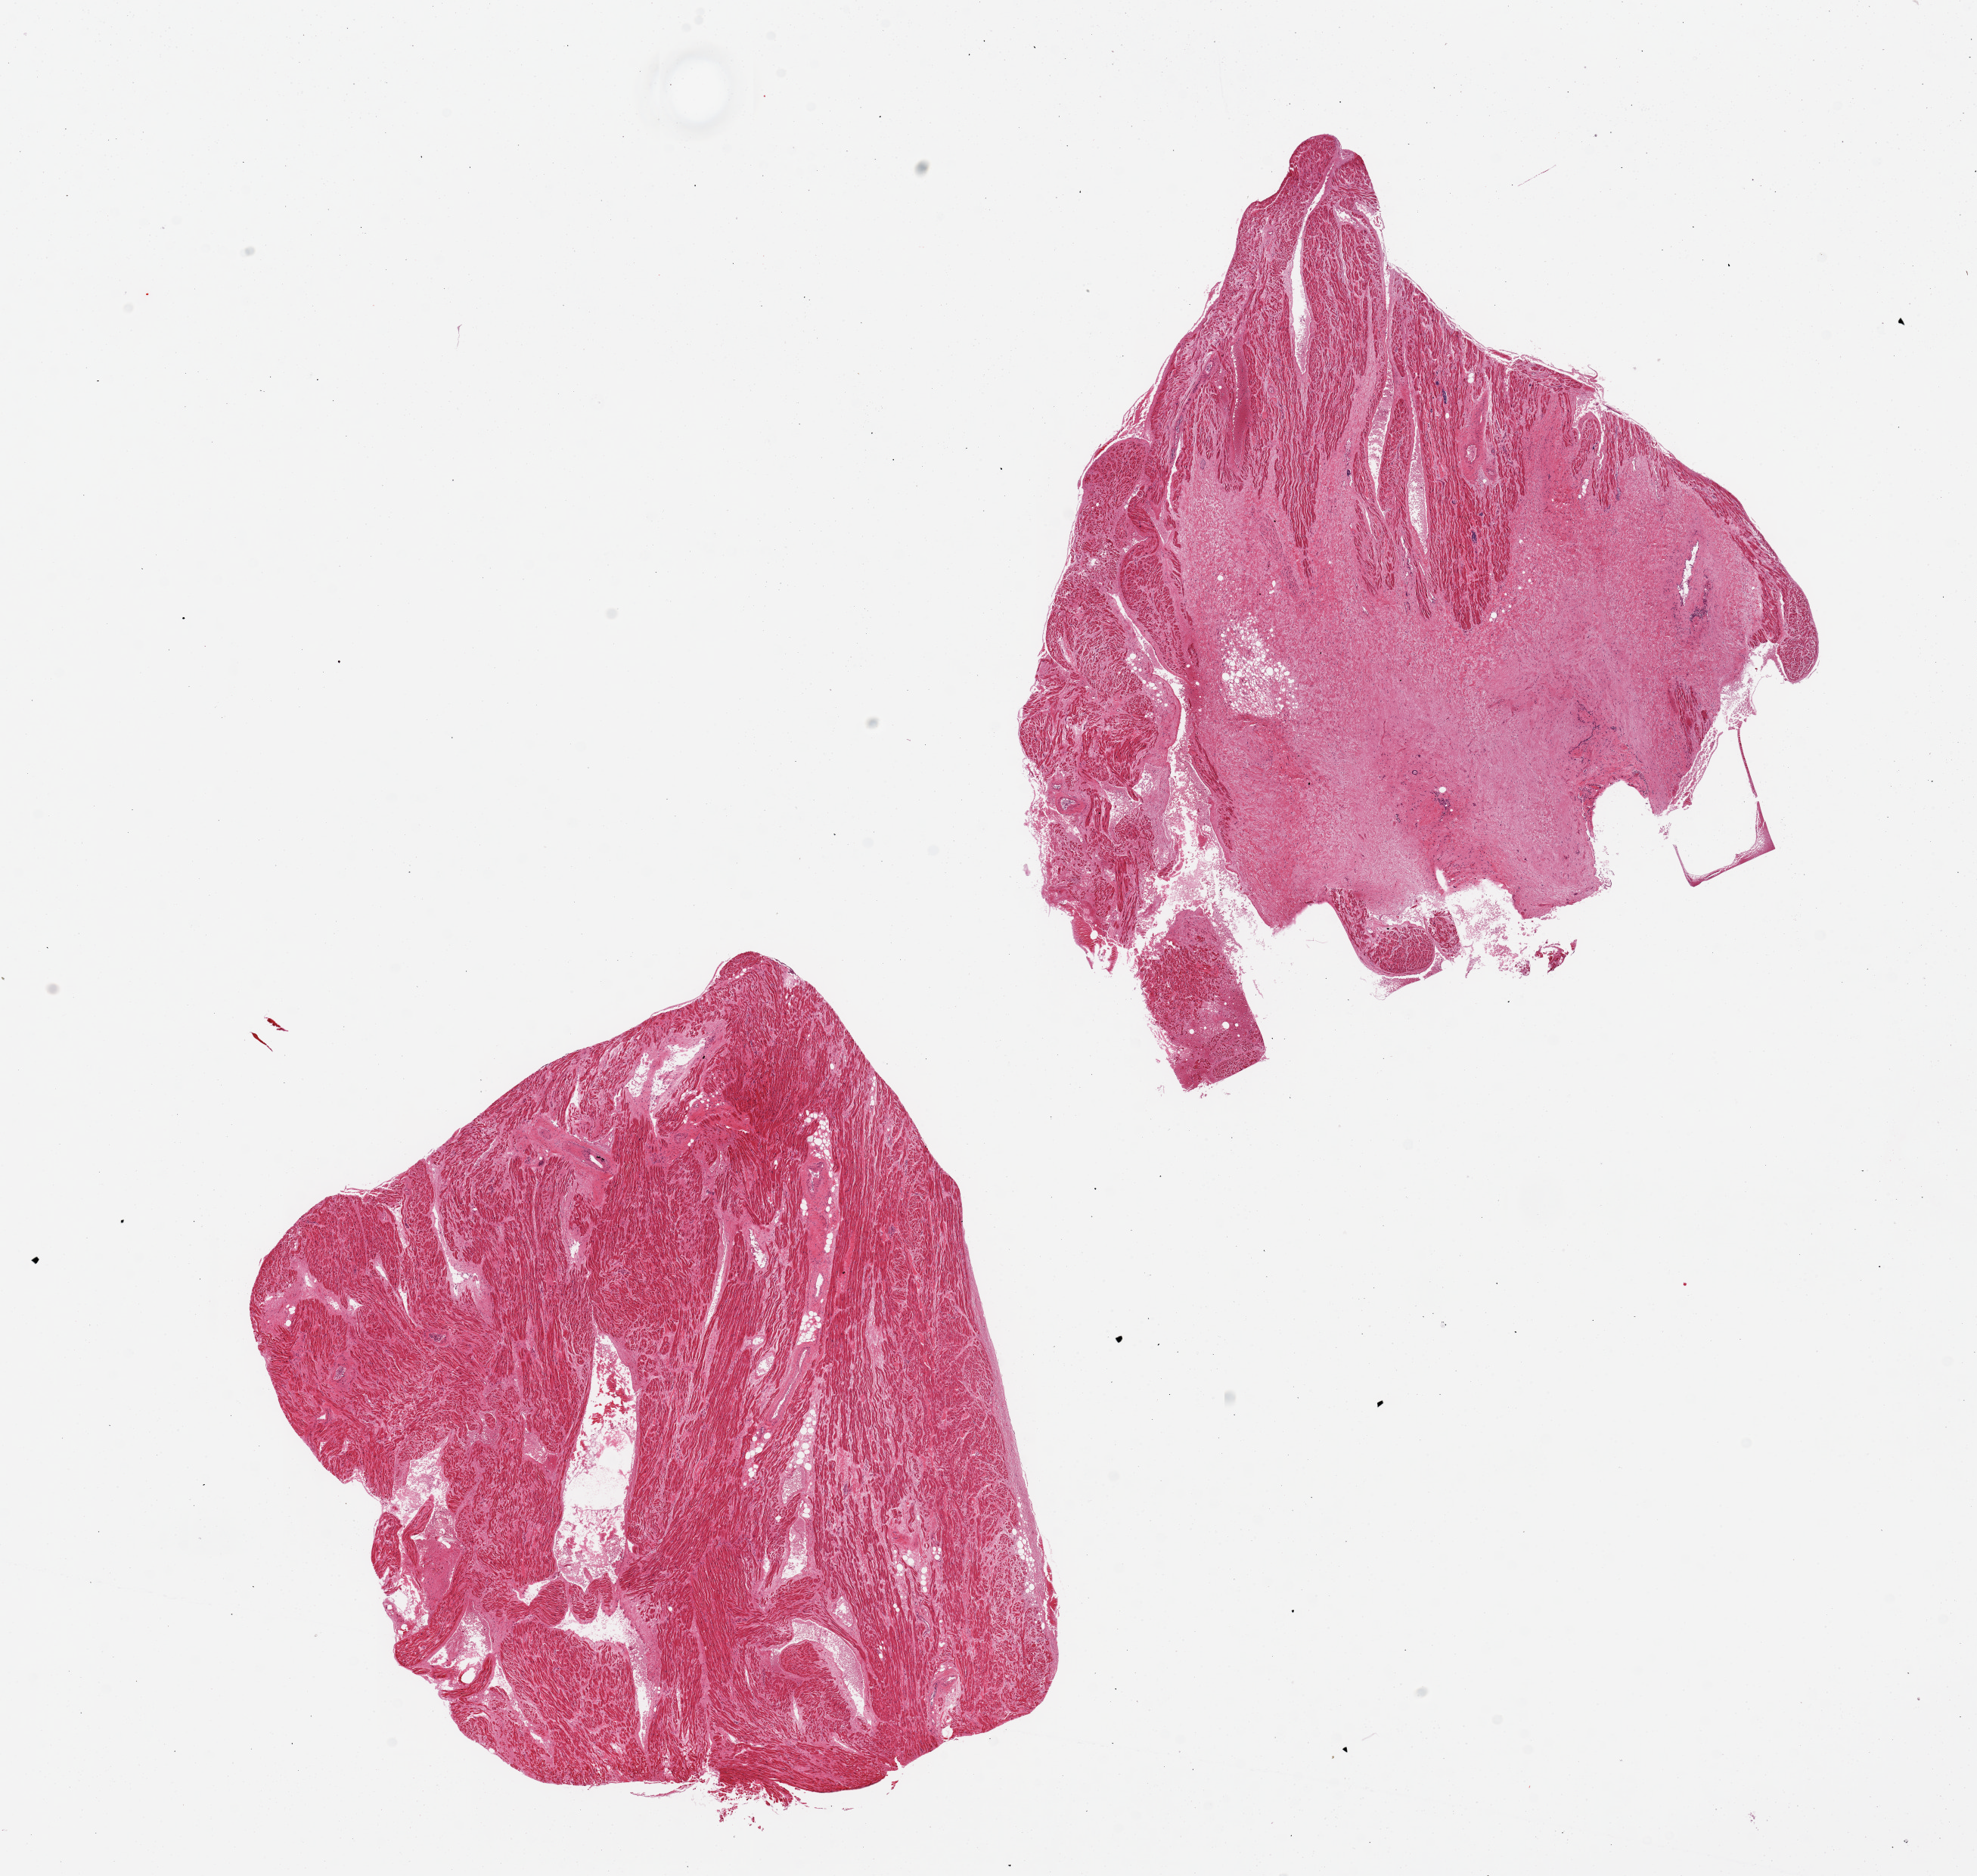
Haematoxylin and eosin whole-slide image, whole scanned area (about 20.7 x 19.6 mm) shown as a low-resolution overview; PAXgene-fixed paraffin-embedded (PFPE) section; section of auricular appendage (target tissue); tissue donor sample. Donor: female.
Reviewer comment on this tissue sample: 2 pieces, interstitial fibrosis and large patch of fibrous tissue.